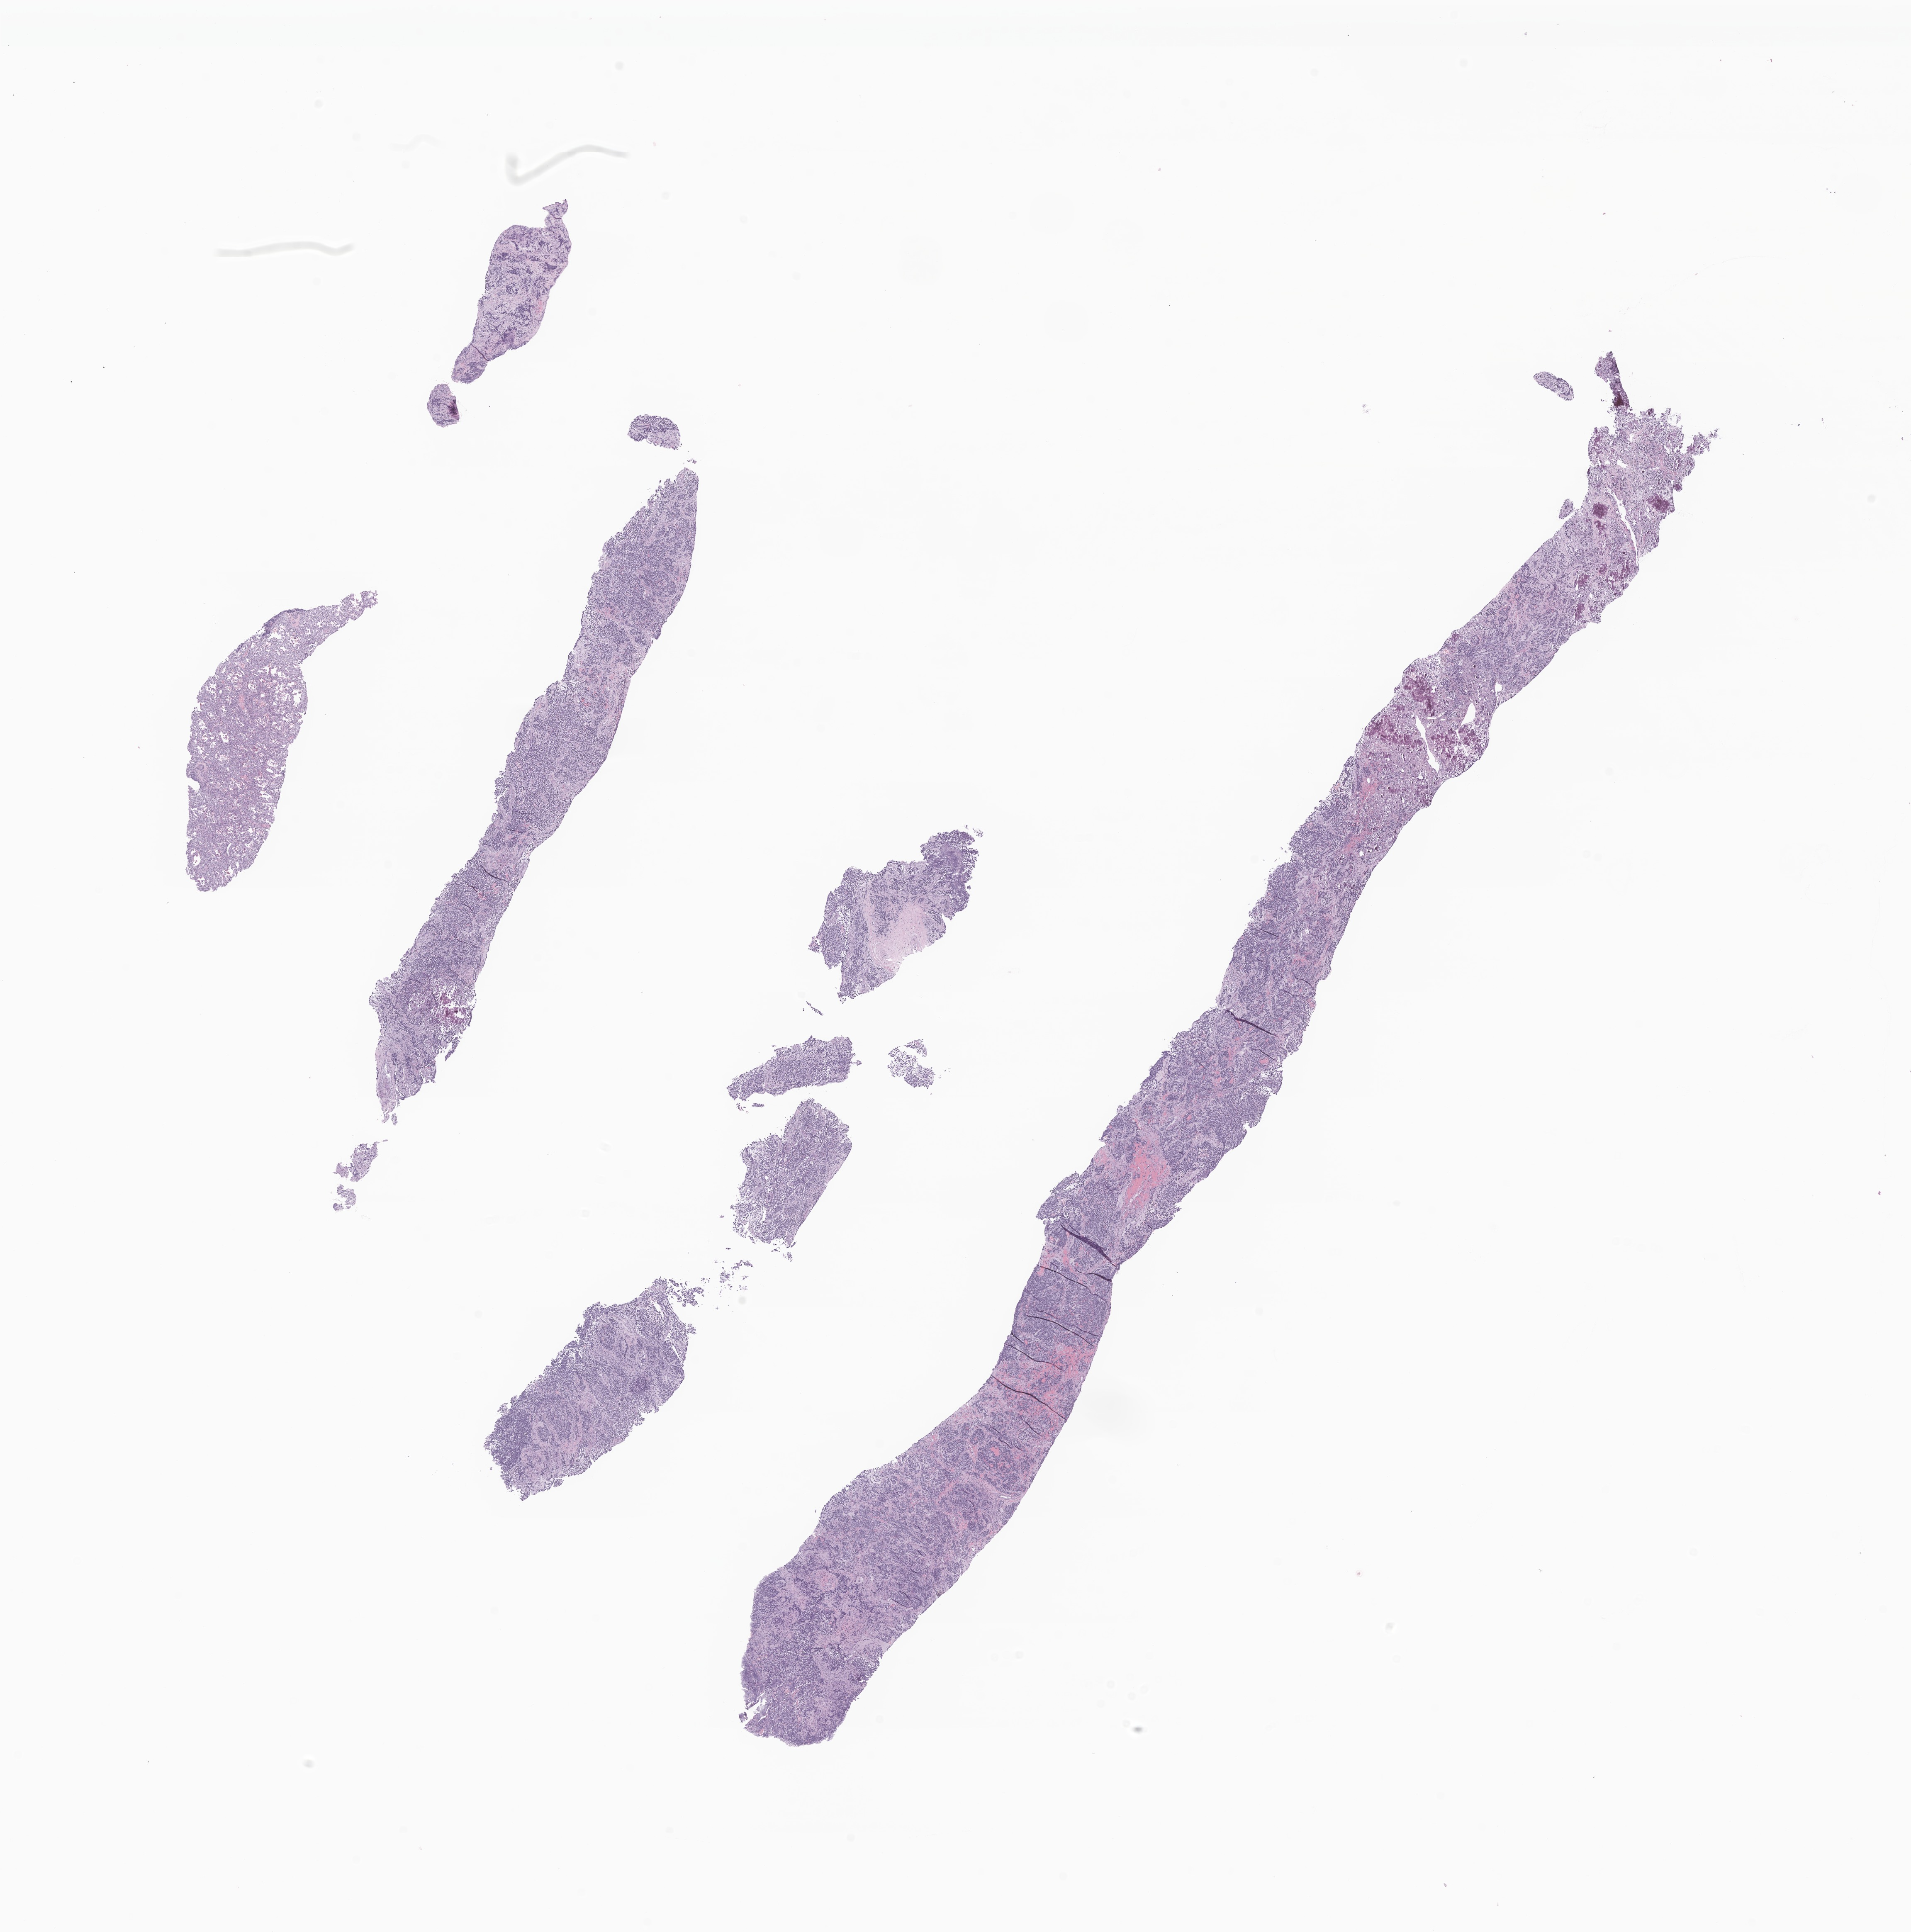
Digitized haematoxylin and eosin-stained section of tumor tissue from the posterior mediastinum — whole scanned area (about 19.4 x 19.6 mm) shown as a low-resolution overview; FFPE section. Patient: female, age 15 days.
Recorded diagnosis: Neuroblastoma, NOS.